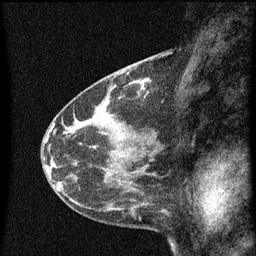
Breast MRI (dynamic contrast-enhanced), one sagittal slice; slice 27 of 60 in the series (ordered by position); dynamic contrast-enhanced series, image 2 of 3 at this slice position (ordered by acquisition); 1.5 T; TE 4.2 ms, TR 8 ms; 2 mm slice thickness; 256 × 256 image matrix, field of view 180 × 180 mm. Female patient, age 41 years.
Structures marked on this image (semi-automatic segmentation, software-assisted and operator-edited):
- analysis volume of interest (the breast-tissue region the enhancement analysis was run in; not a lesion): bounding box [x1, y1, x2, y2] px = [130, 78, 151, 99]
- tumour enhancement mask (voxels above the 70 % enhancement threshold inside the analysis volume of interest): [140, 78, 151, 95]